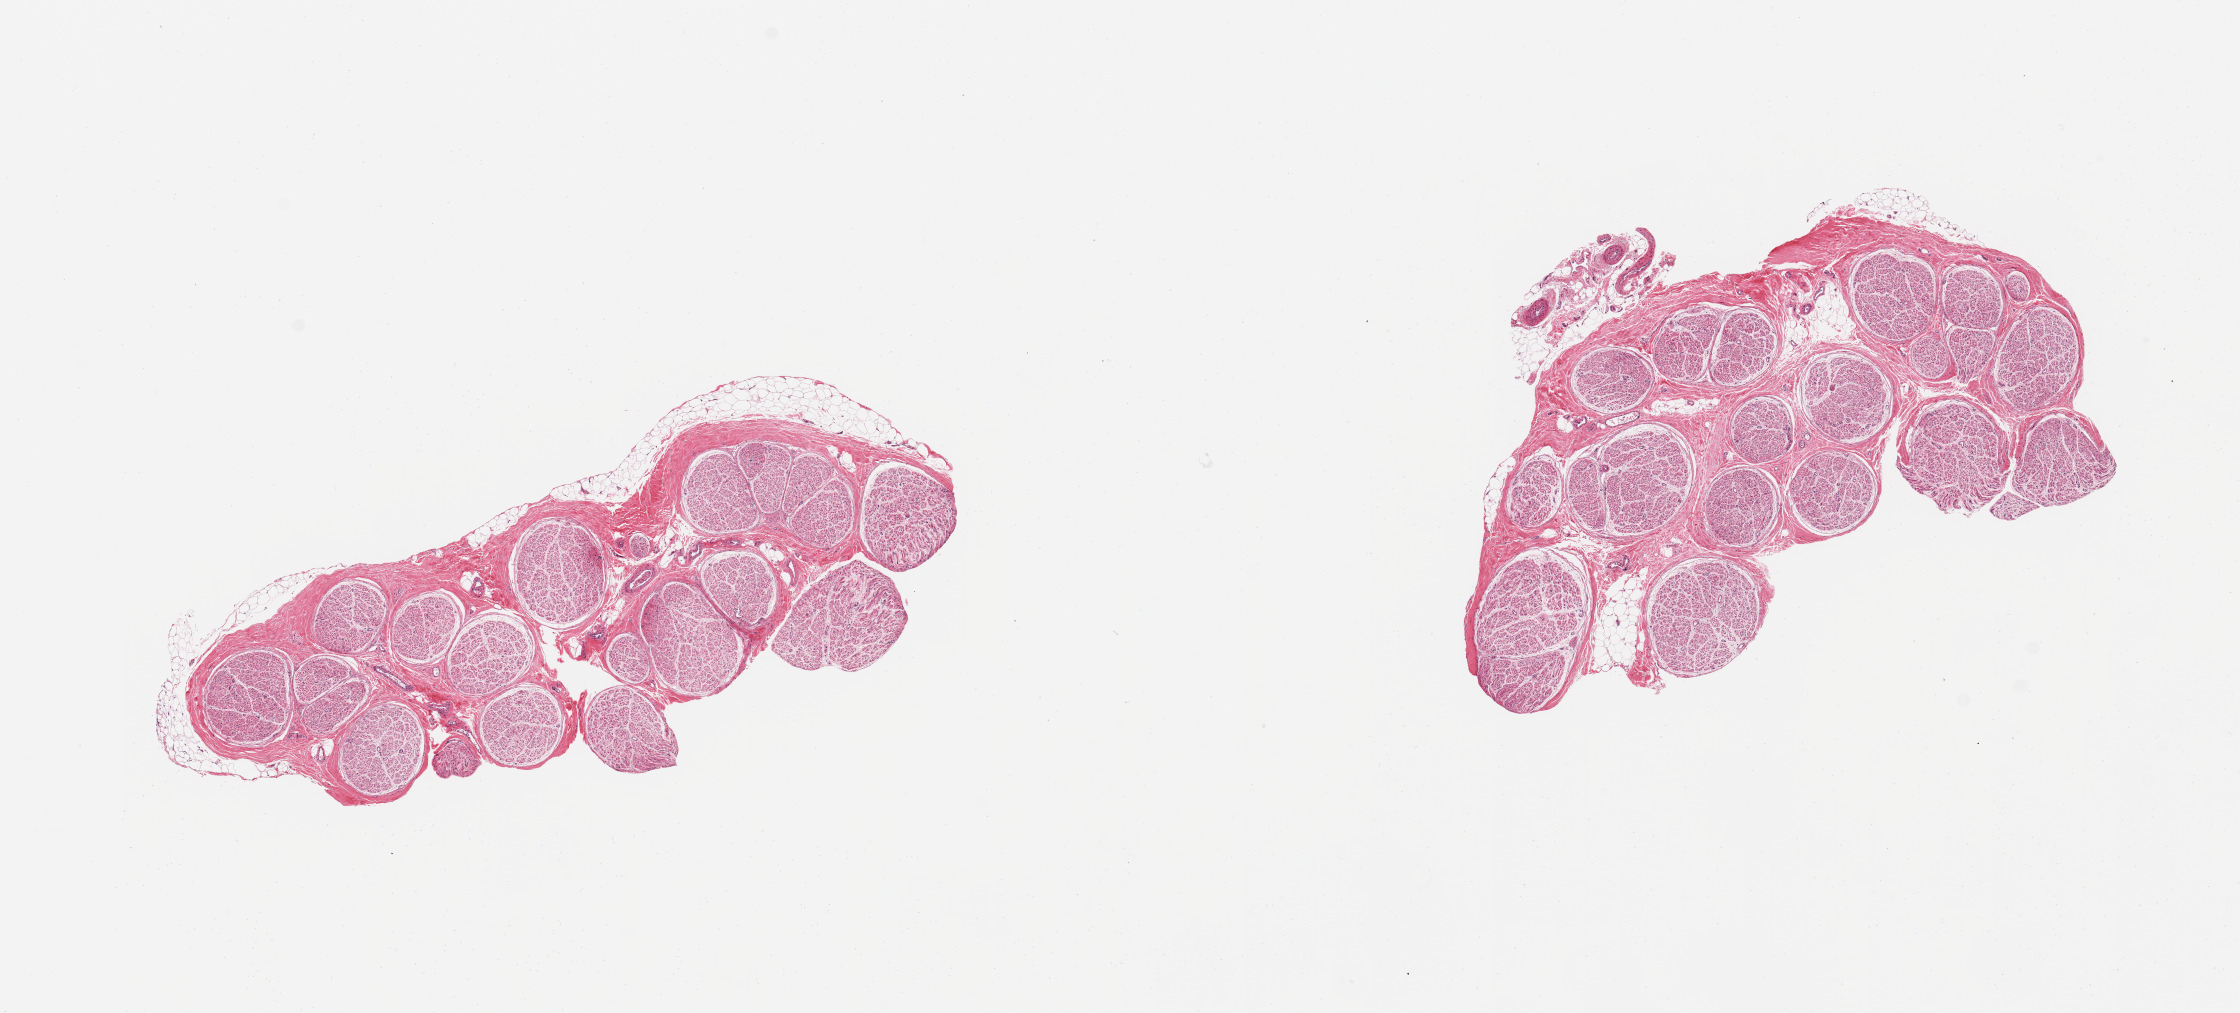
Digitized haematoxylin and eosin-stained section — low-resolution overview of the scanned area, about 17.7 x 8.0 mm. PAXgene-fixed paraffin-embedded (PFPE) section. Section of tibial nerve (target tissue). Tissue donor sample.
Pathologist's review note for this sample: 2 pieces; 10% external fat.